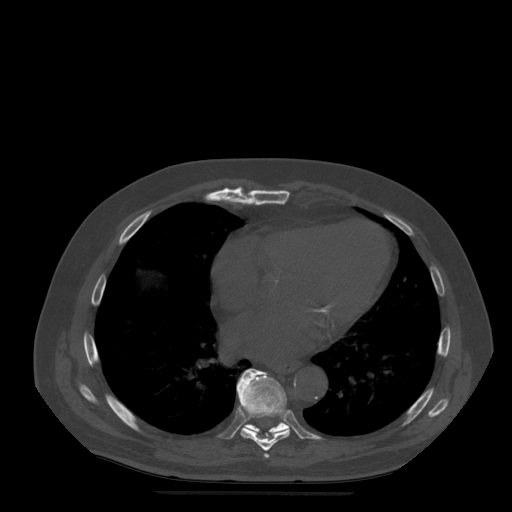
CT including the spine, one axial slice; position 305 of 522 along the scan axis; bone window (W 1800 / L 400 HU); 1.25 mm slice thickness; 512 × 512 image matrix, field of view 420 × 420 mm. Patient age 72 years. Case-level facts recorded for this patient, not image findings: primary cancer: prostate.
Structures marked on this image (semi-automatically segmented with operator editing):
- T7 vertebra: bounding box <264,454,270,459> (left, top, right, bottom; pixels)
- T8 vertebra: <237,371,290,451>
- T9 vertebra: <237,369,289,435>